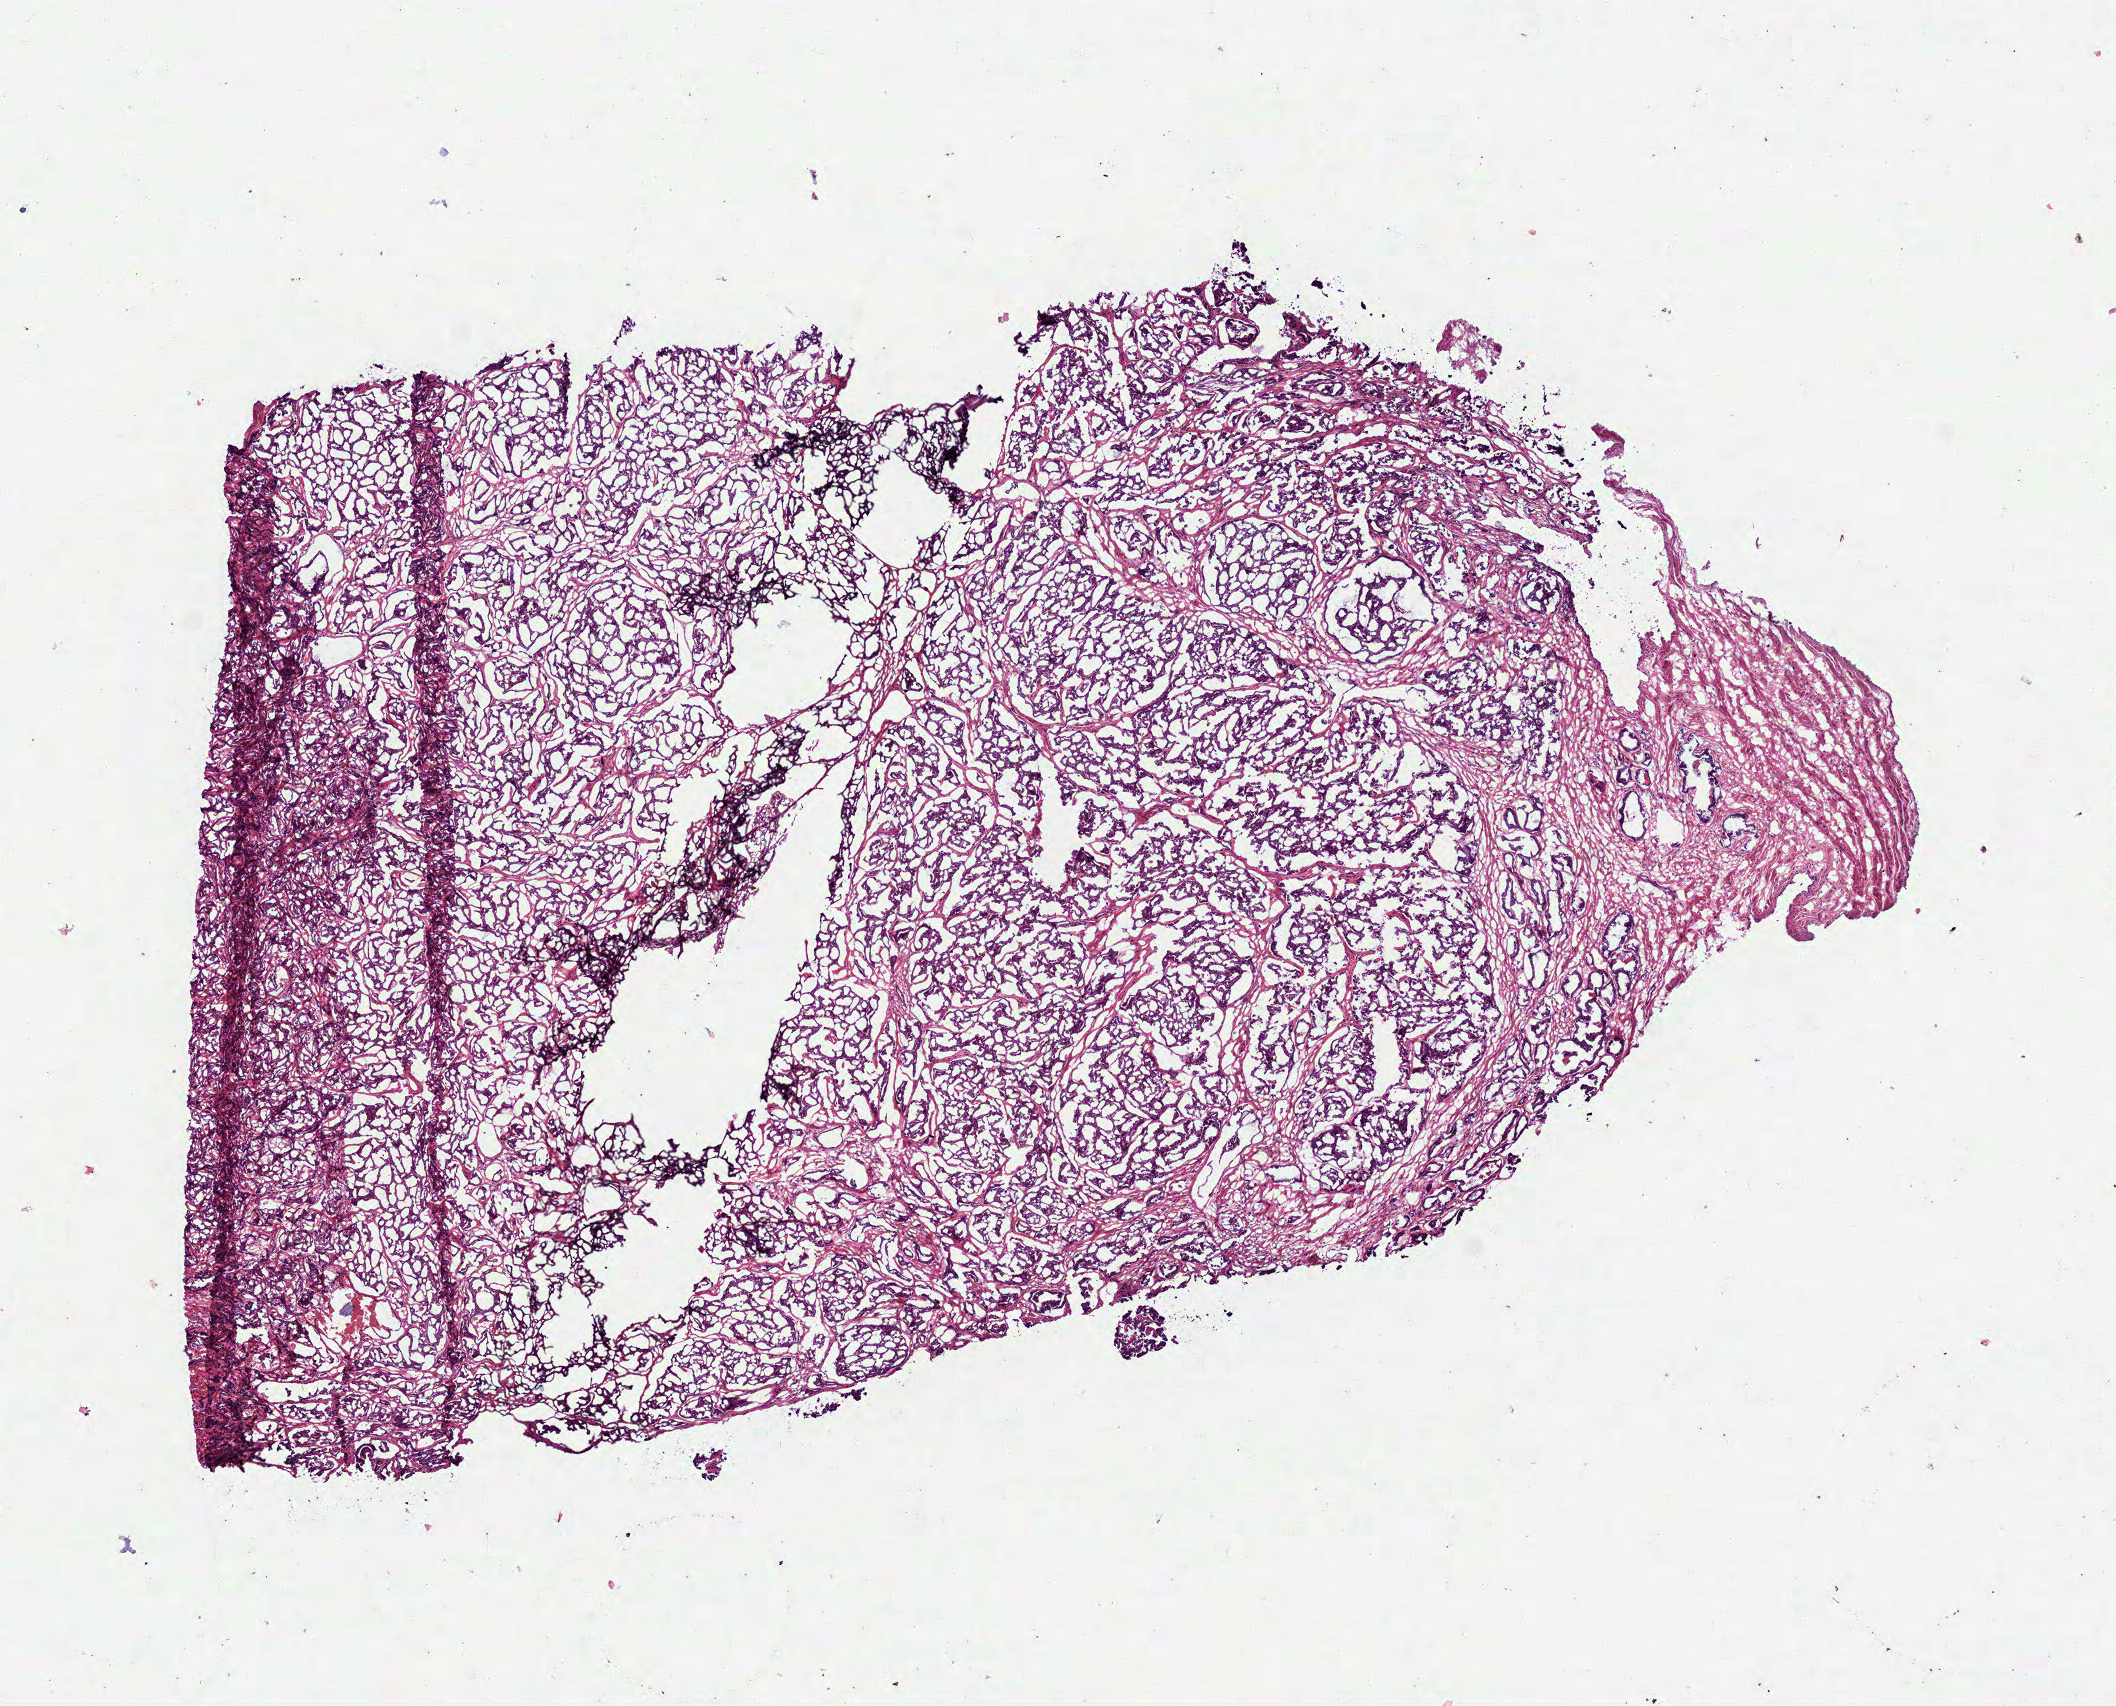
Digitized H&E-stained tissue section (whole slide) — shown as a low-resolution overview of the whole scanned area (about 8.5 x 6.9 mm), frozen section, primary tumour sample from the prostate. Male, age 55 years at initial diagnosis. Gleason score: 7 (4+3). Composition of this section per pathologist review: tumour cells 80%, tumour nuclei 80%, normal cells 10%, stromal cells 10%, necrosis 0%. Infiltration values recorded for this section: lymphocyte infiltration 0%, monocyte infiltration 0%, neutrophil infiltration 0%.
- pathologic diagnosis: Acinar cell carcinoma (prostate gland)
- laterality: bilateral
- lymph nodes positive (case pathology): 0 of 21 examined